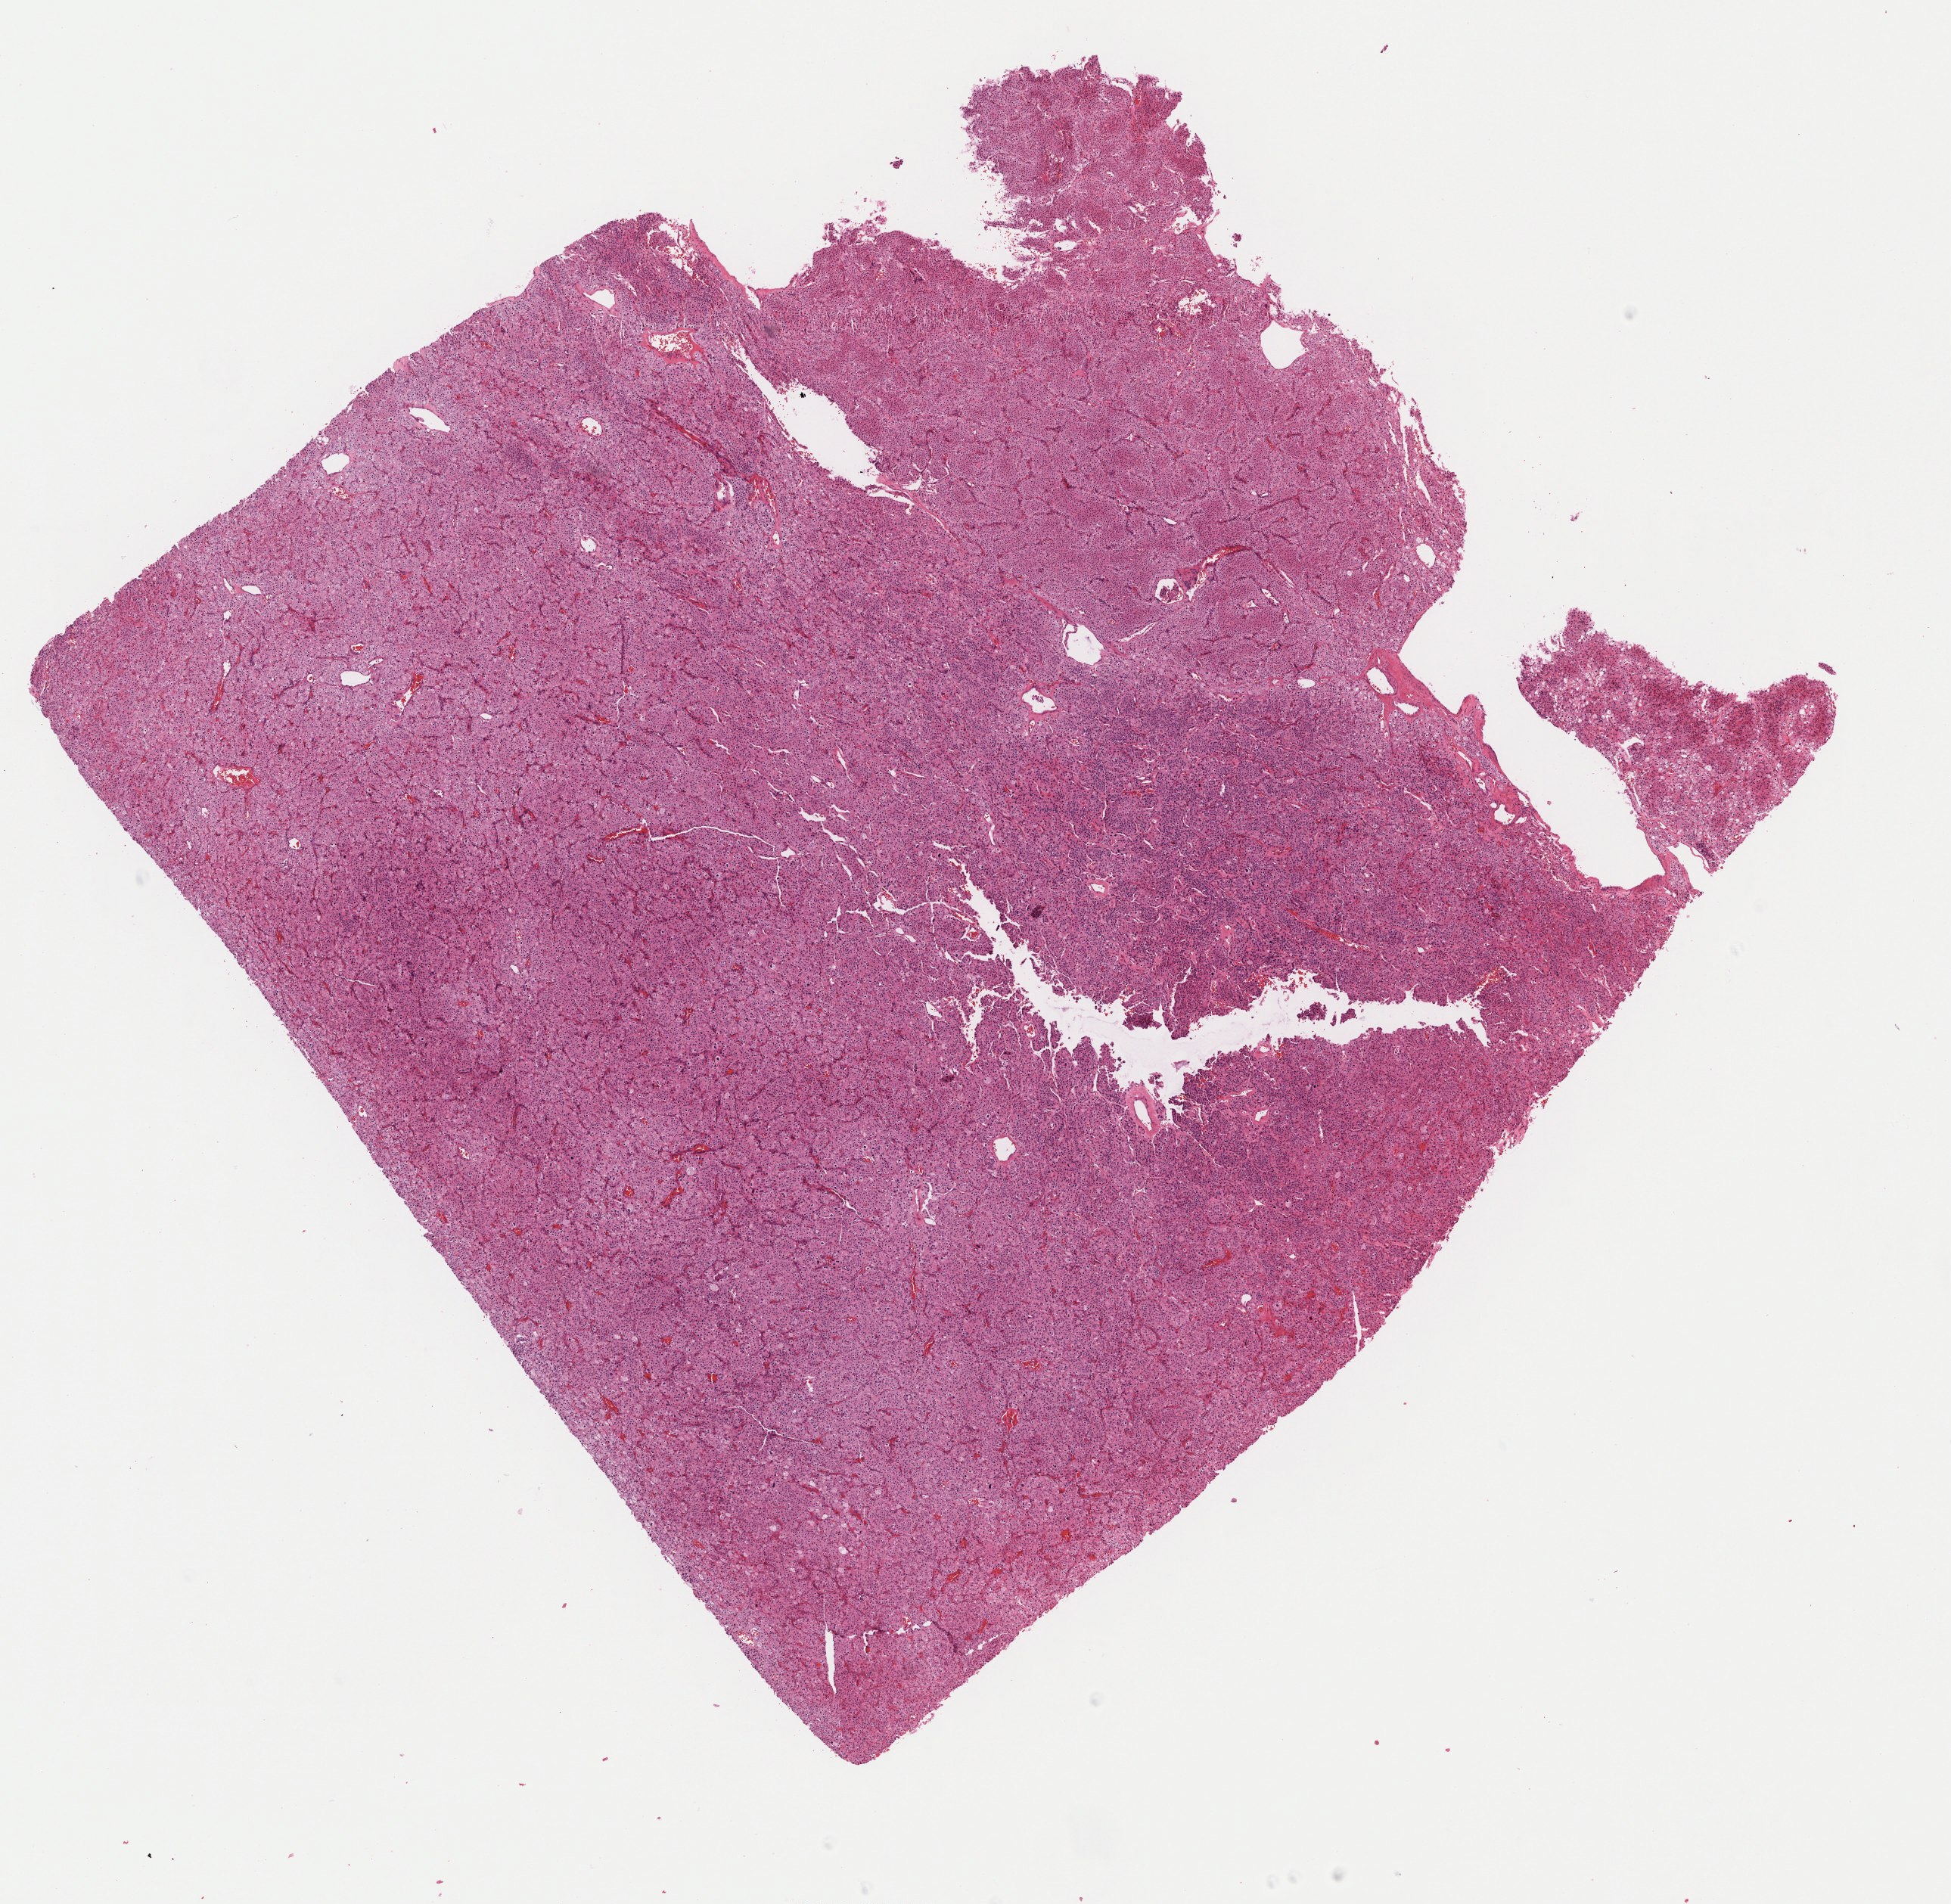
Digitized H&E-stained tissue section (whole slide), whole scanned area (about 10.4 x 10.1 mm, slide scanned at 40x) shown as a low-resolution overview, FFPE section, kidney, primary tumour sample. Patient: female, age at initial diagnosis 86 years.
Diagnosis: Renal cell carcinoma, chromophobe type.